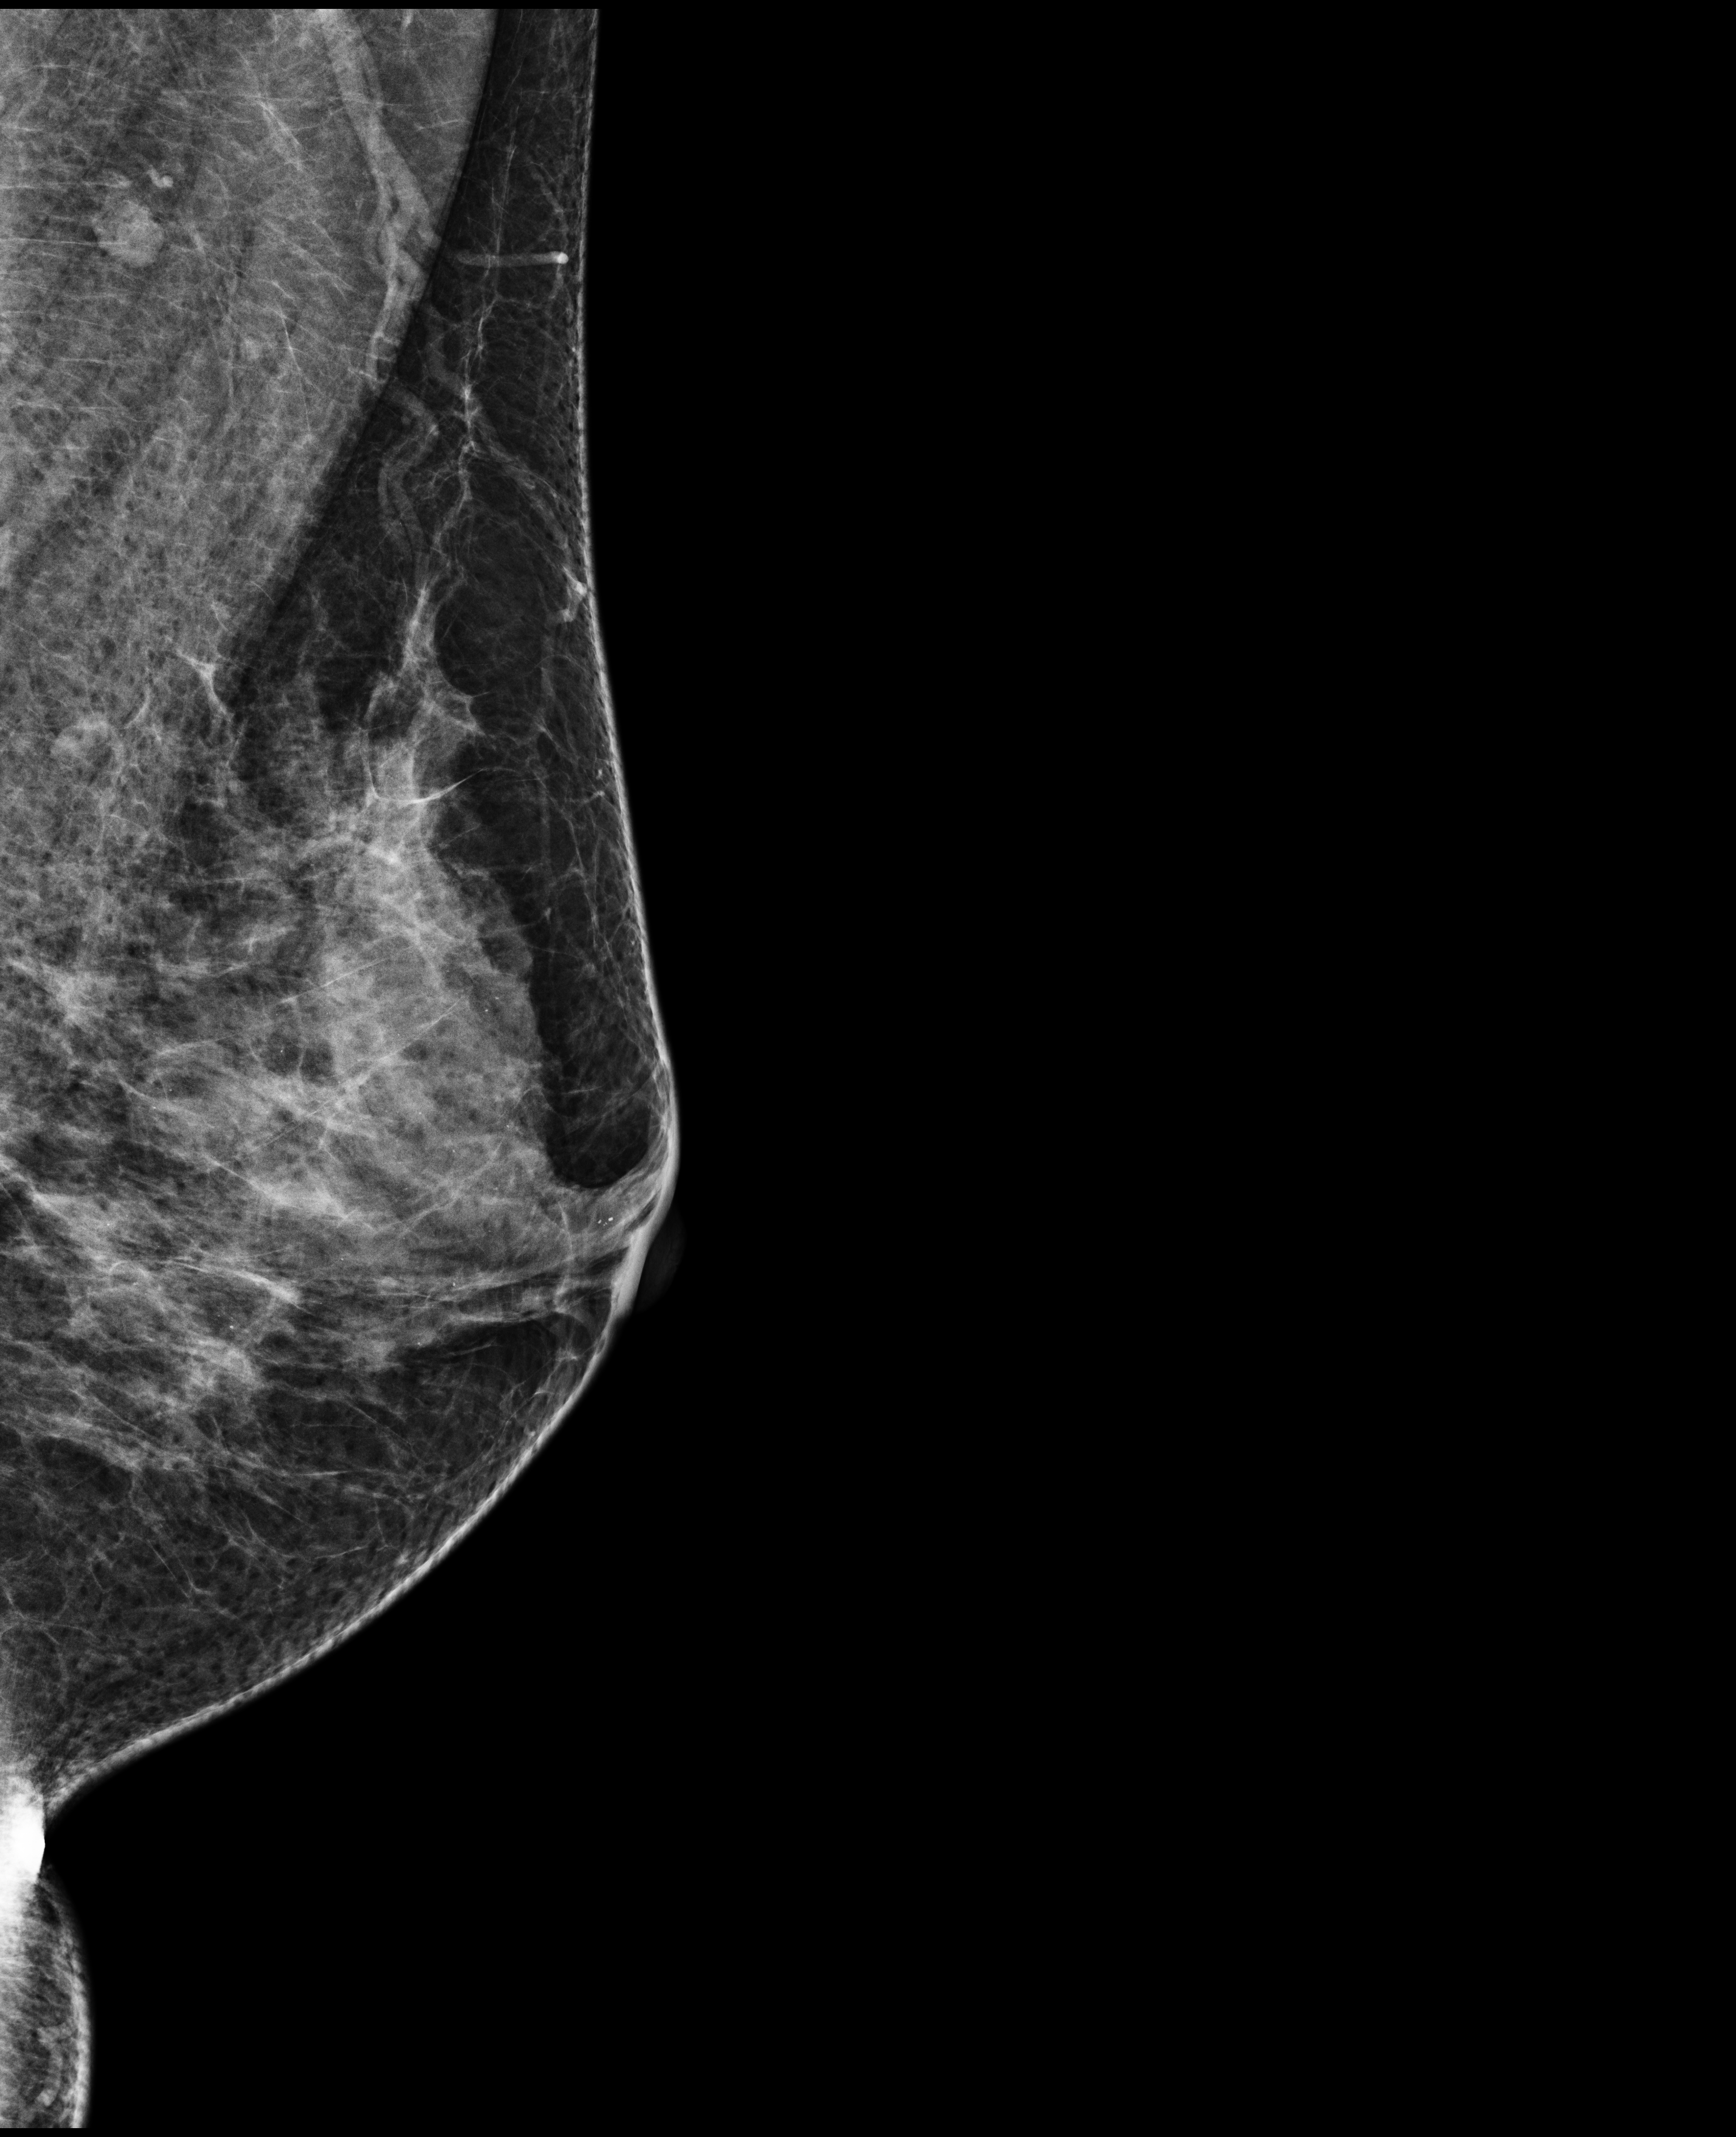
Annual screening mammography examination. Female patient, age 49 years.
Image type: full-field digital mammogram. Breast: left. Projection: MLO view.